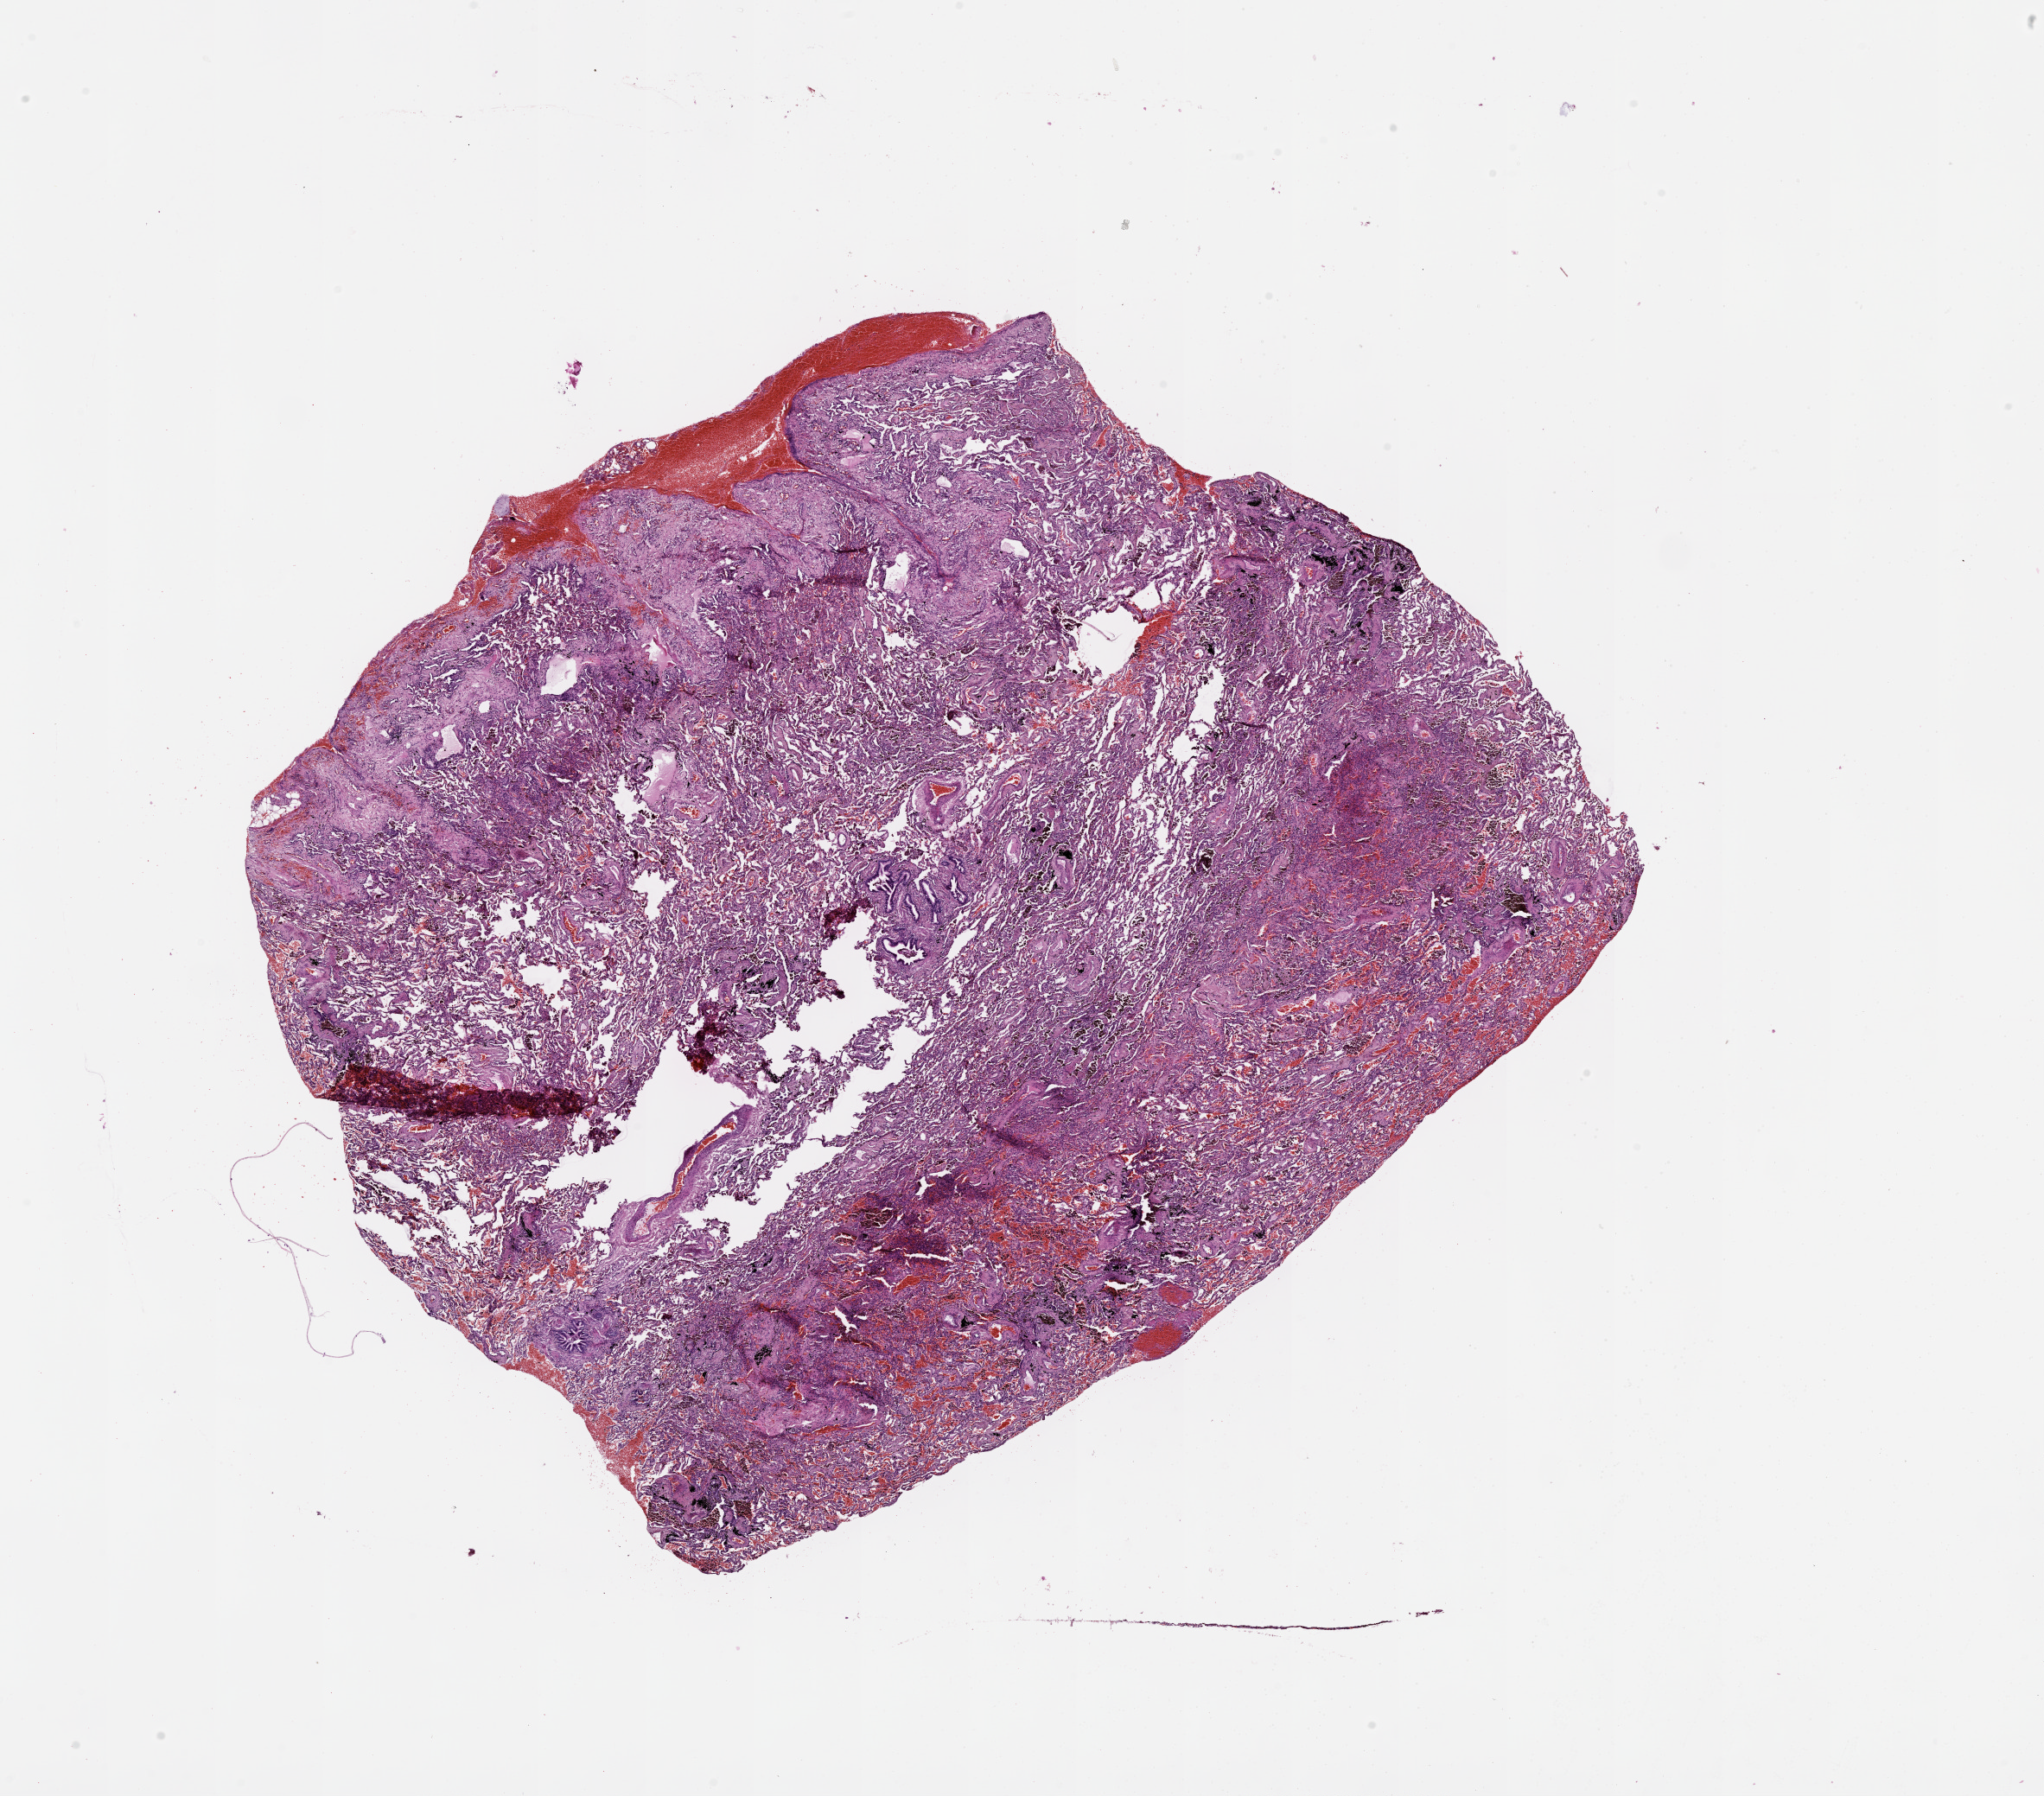
Whole-slide histology image, Hematoxylin and eosin (H&E) stained — shown as a low-resolution overview of the whole scanned area (about 19.0 x 16.7 mm, slide scanned at 20x). Lung, normal (non-tumour) tissue. Patient: female, age 56 years.
This section: normal (non-tumour) tissue from the same patient. Patient diagnosis (cohort enrolment): squamous cell carcinoma (lung).